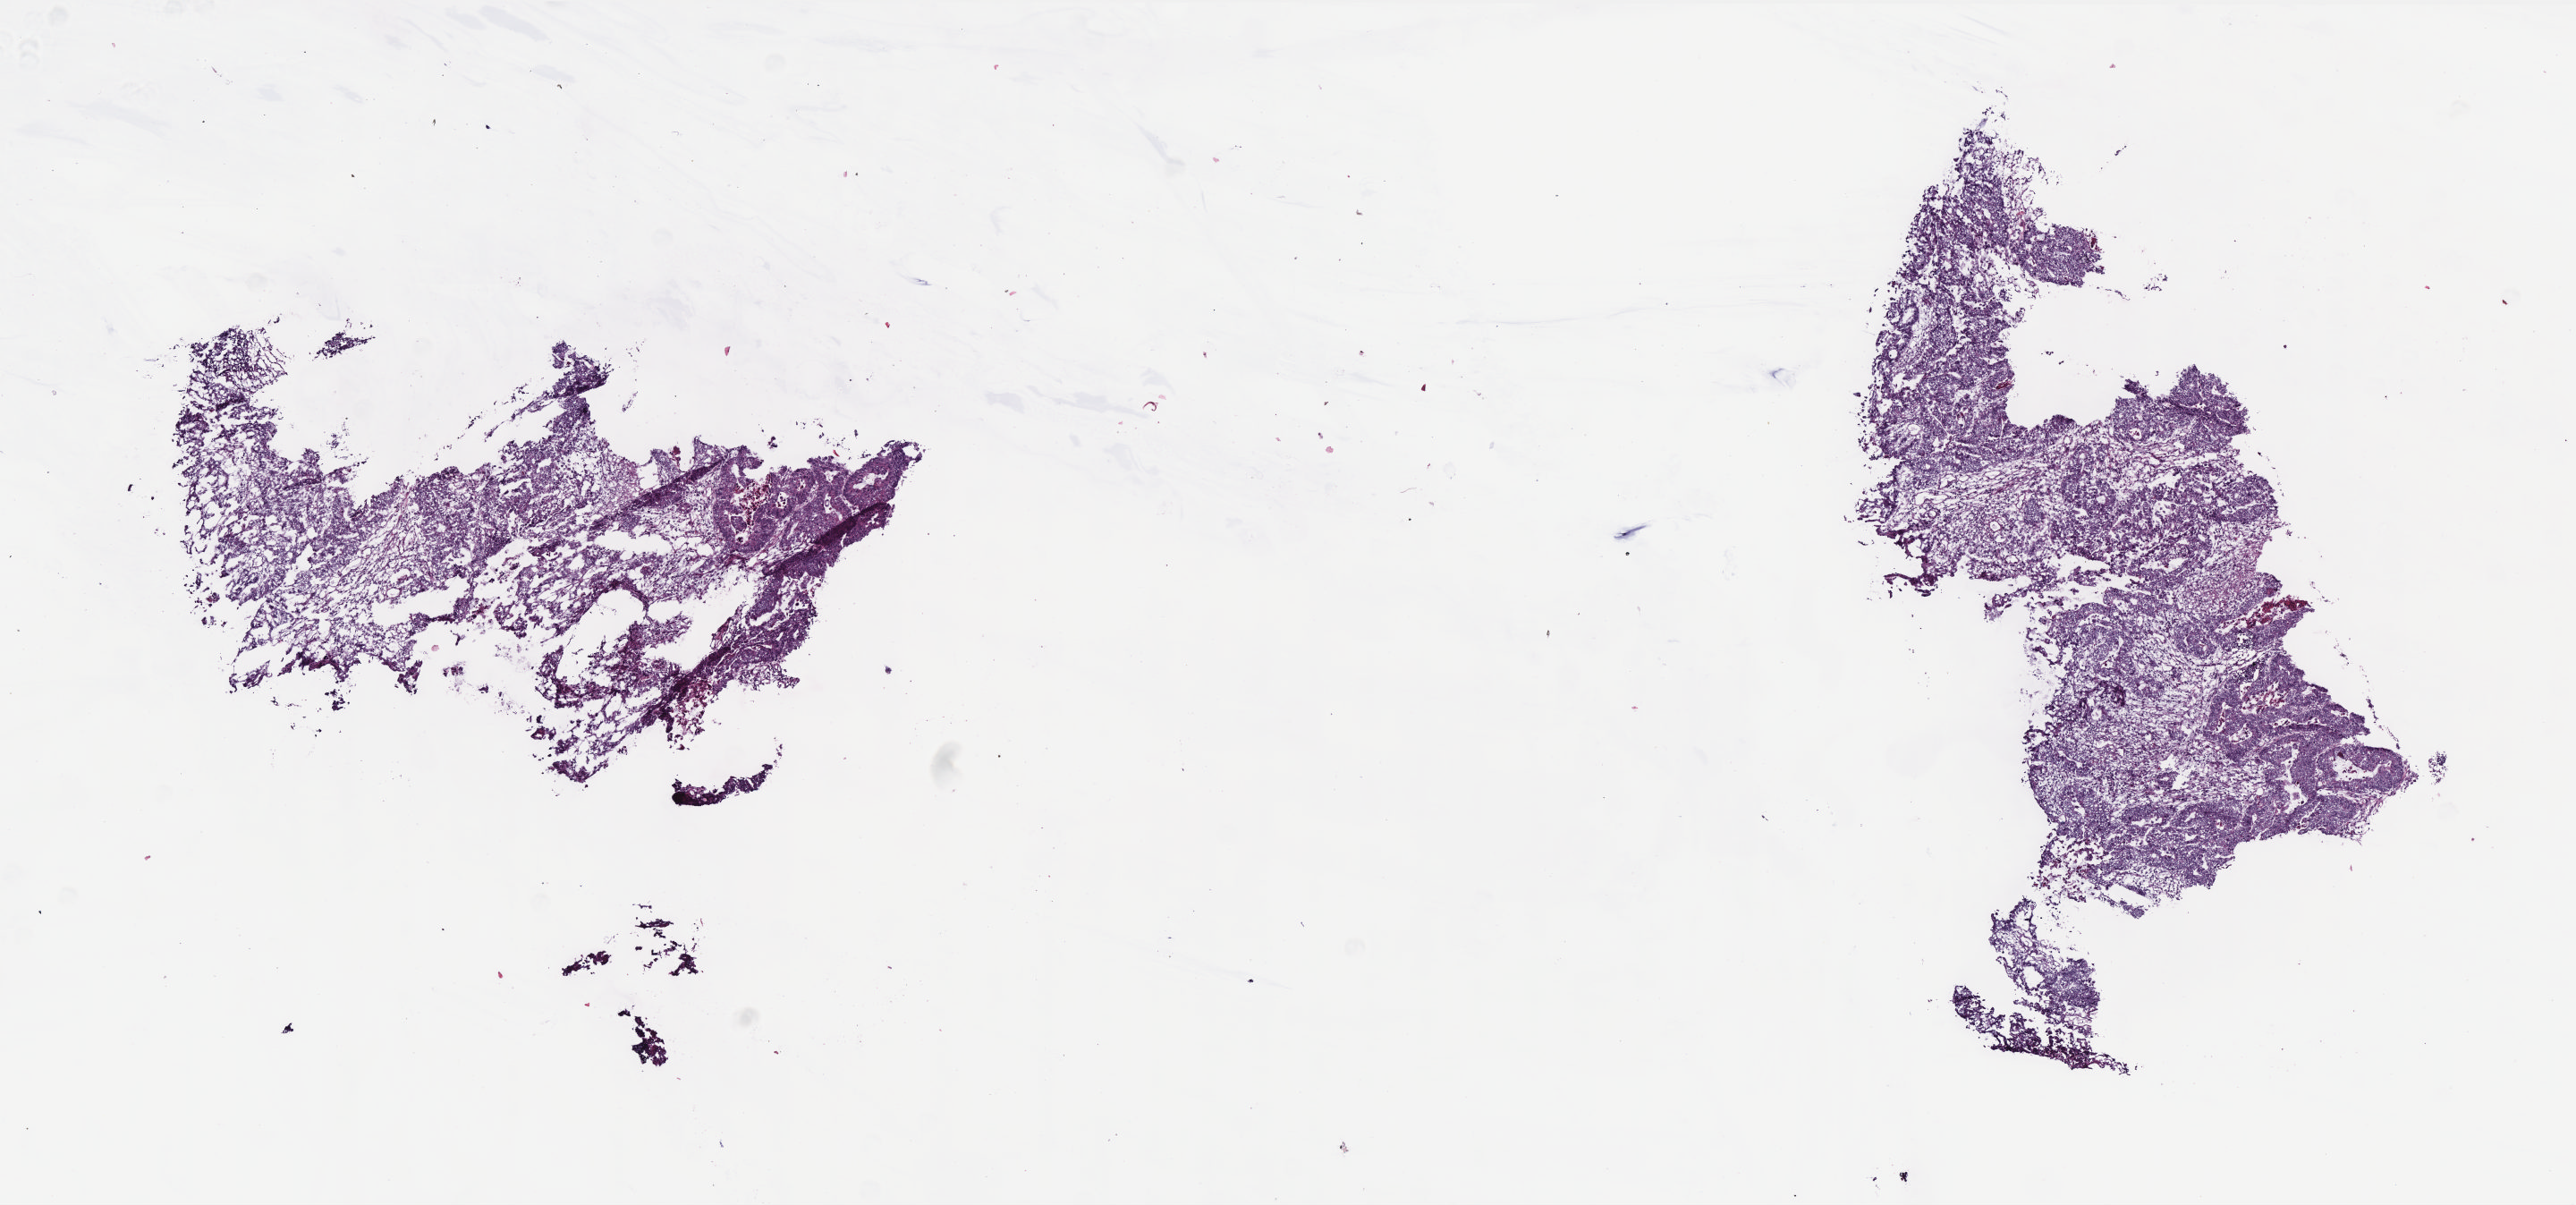
H&E-stained whole-slide image — shown as a low-resolution overview of the whole scanned area (about 11.5 x 5.4 mm, from a 40x scan), frozen section, sample: primary tumour, rectum. Male patient; age at initial diagnosis 68 years. Composition of this section per pathologist review: tumour cells 85%, tumour nuclei 85%, normal cells 0%, stromal cells 13%, necrosis 2%. Infiltration values recorded for this section: lymphocyte infiltration 8%, monocyte infiltration 2%, neutrophil infiltration 1%.
• AJCC pathologic stage: IIA (6th edition)
• lymph nodes positive (case pathology): 0 of 31 examined
• TNM: T3 N0 M0
• histologic diagnosis: Adenocarcinoma, NOS